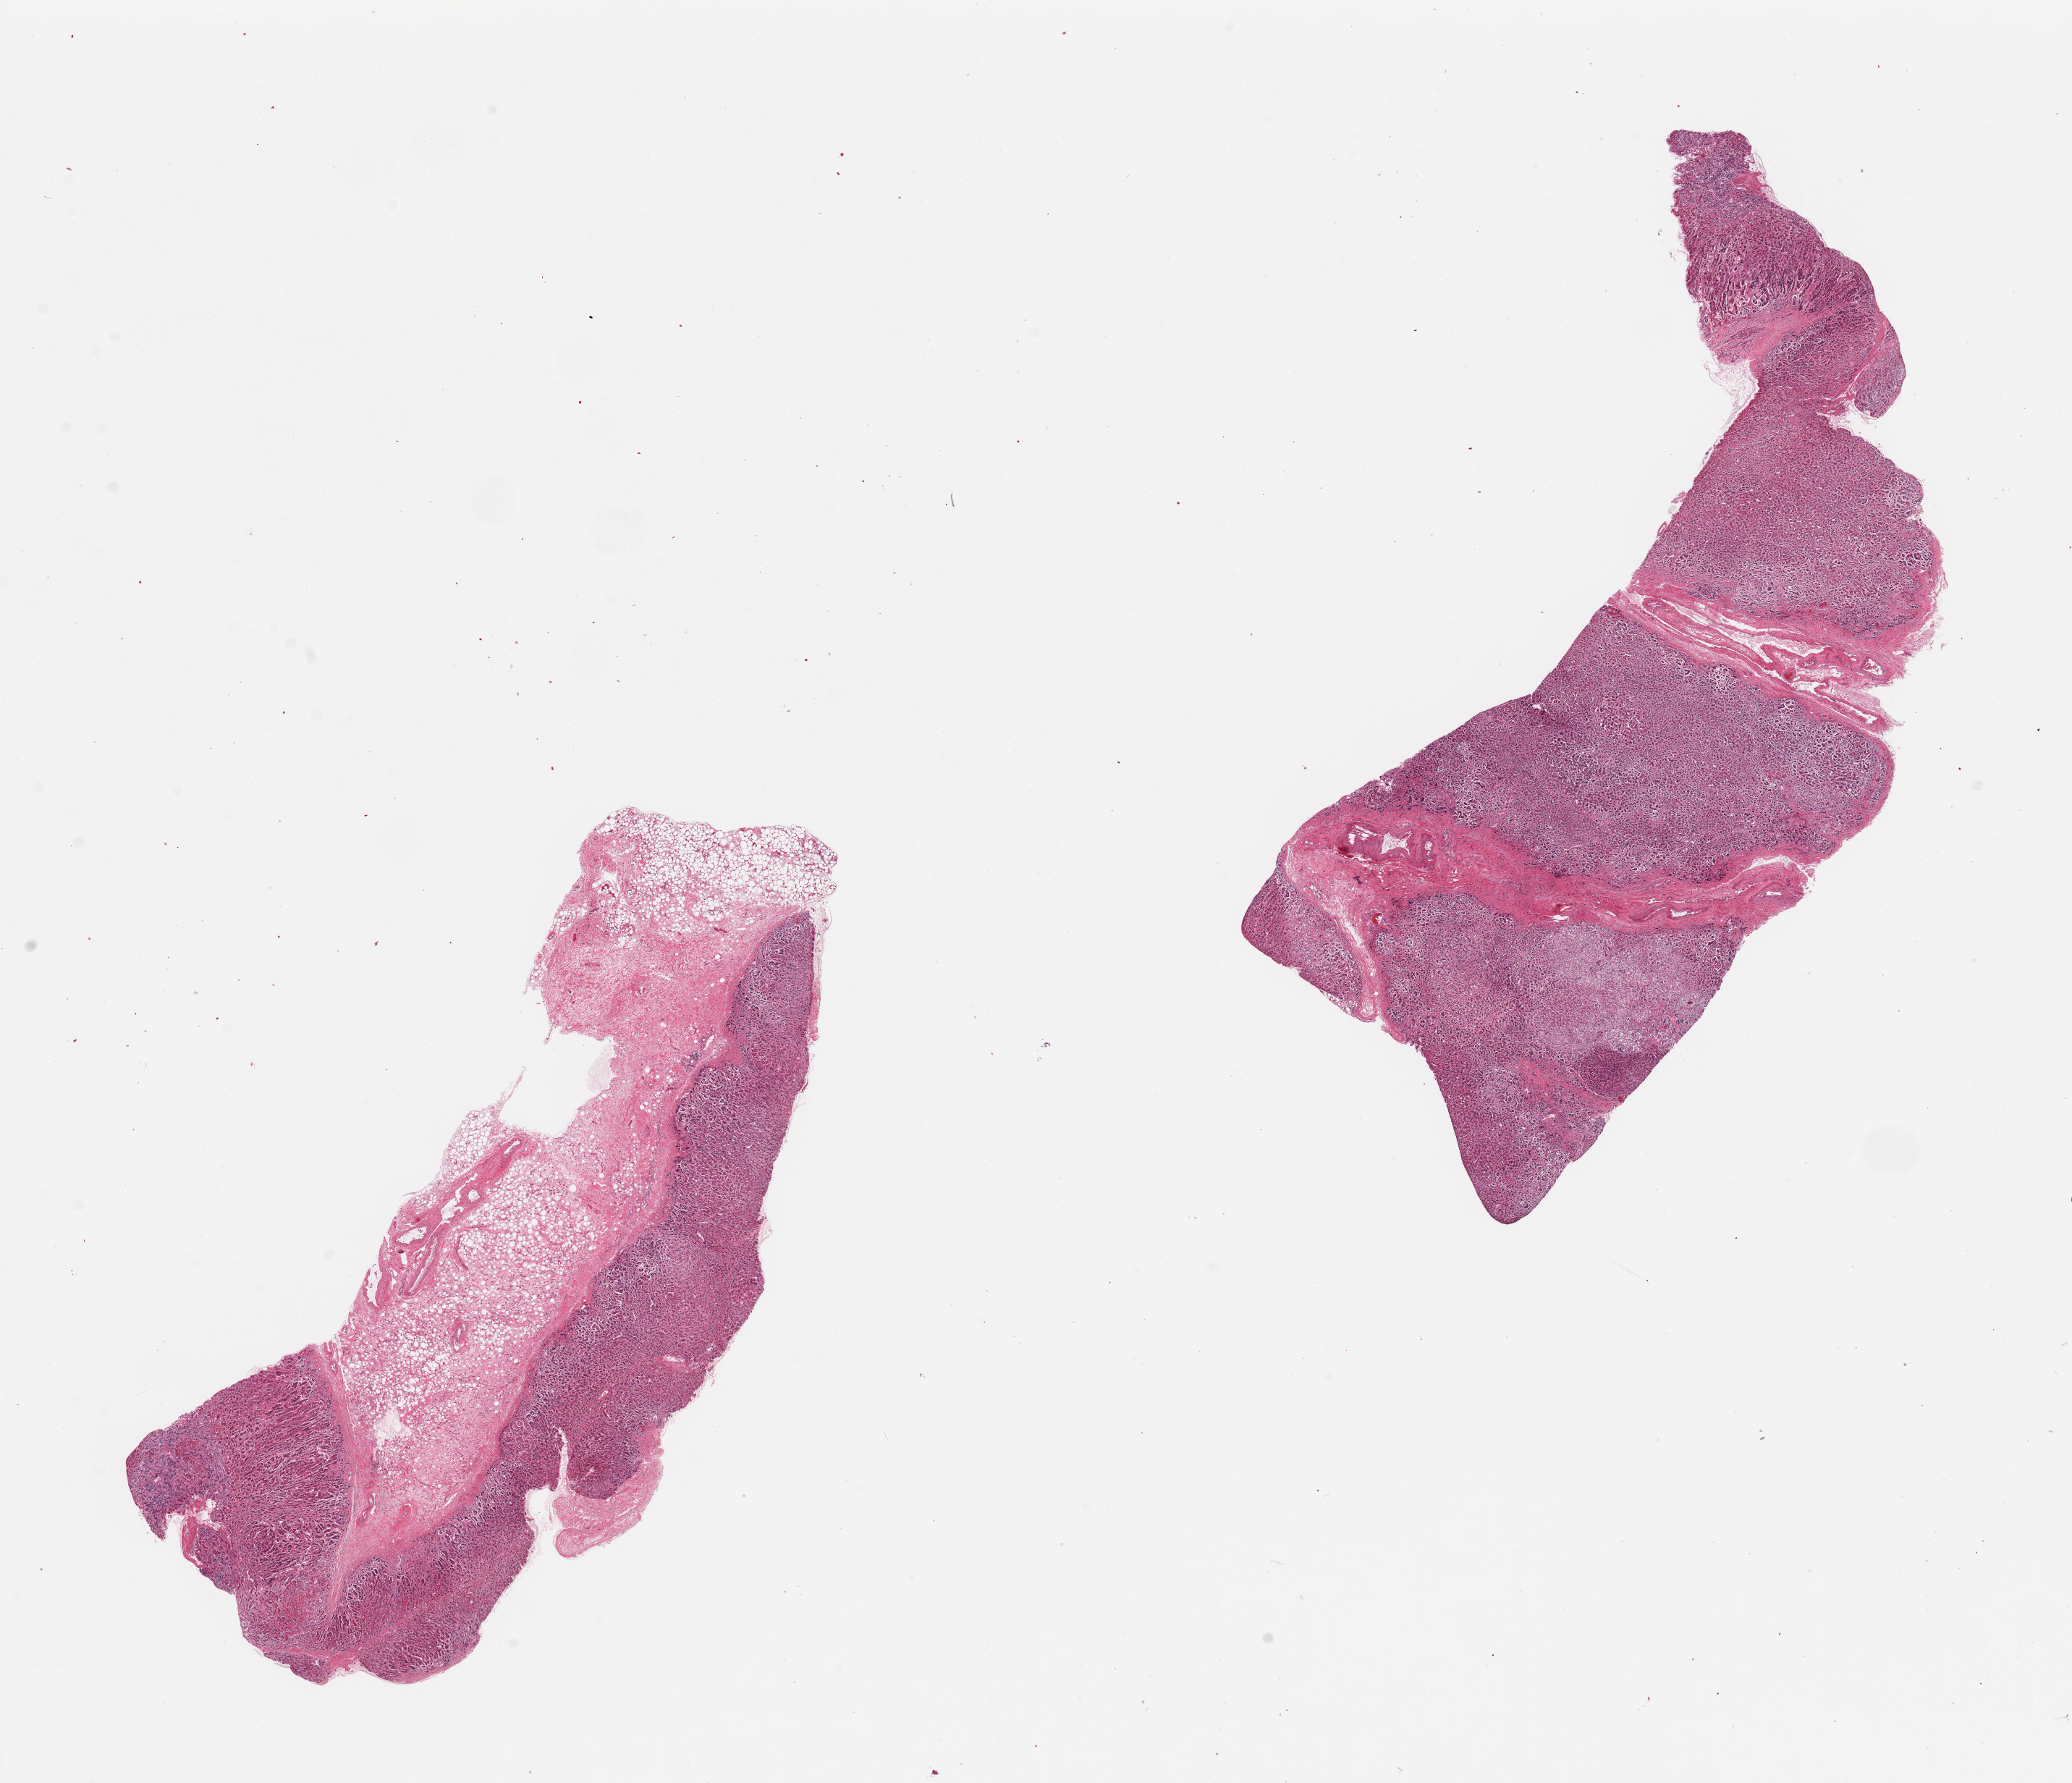
Whole-slide image, H&E stain, brightfield — shown as a low-resolution overview of the whole scanned area (about 22.6 x 19.5 mm, acquisition: 20x scan). PAXgene-fixed paraffin-embedded (PFPE) section. Section of adrenal gland (target tissue). Tissue donor sample. Donor: male.
Reviewer comment on this tissue sample: 2 pieces; 1 piece 60% external fat; autolysis makes it of borderline value.